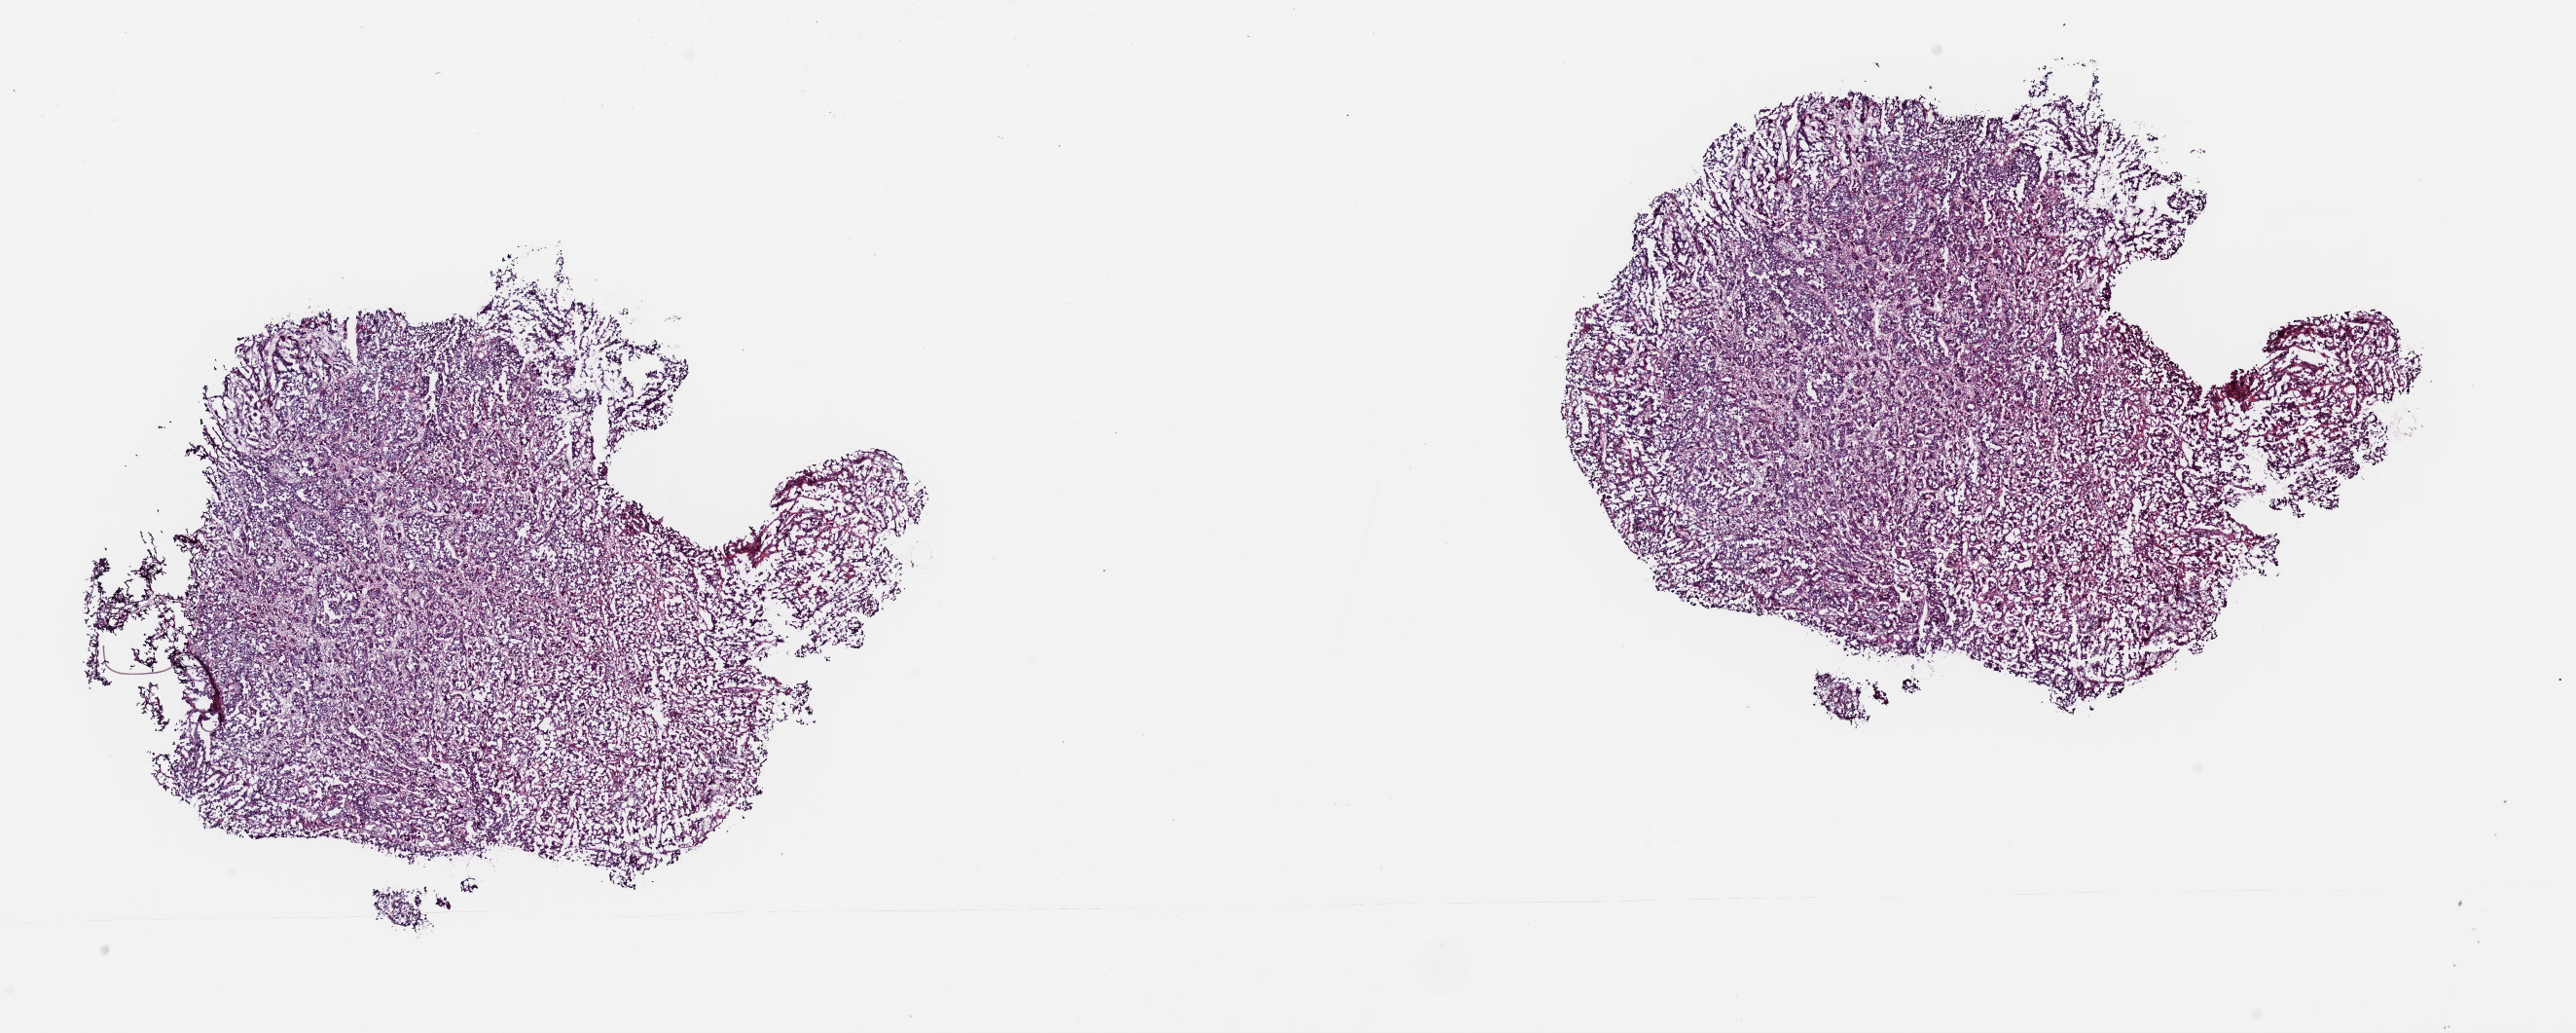
Hematoxylin and eosin (H&E) stained whole-slide image — low-resolution overview of the scanned area, about 20.9 x 8.4 mm; frozen section from the top of the tissue portion; primary tumour sample from the bladder. Male, age 66 years at initial diagnosis. Histologic grade: high grade. Composition of this section per pathologist review: tumour cells 100%, tumour nuclei 90%, normal cells 0%, stromal cells 0%, necrosis 0%. Inflammatory infiltration, as recorded: lymphocyte infiltration 3%, monocyte infiltration 0%, neutrophil infiltration 0%.
Lymph nodes positive (case pathology): 1 of 17 examined. Histologic diagnosis: Transitional cell carcinoma. AJCC pathologic stage: IV (7th edition).